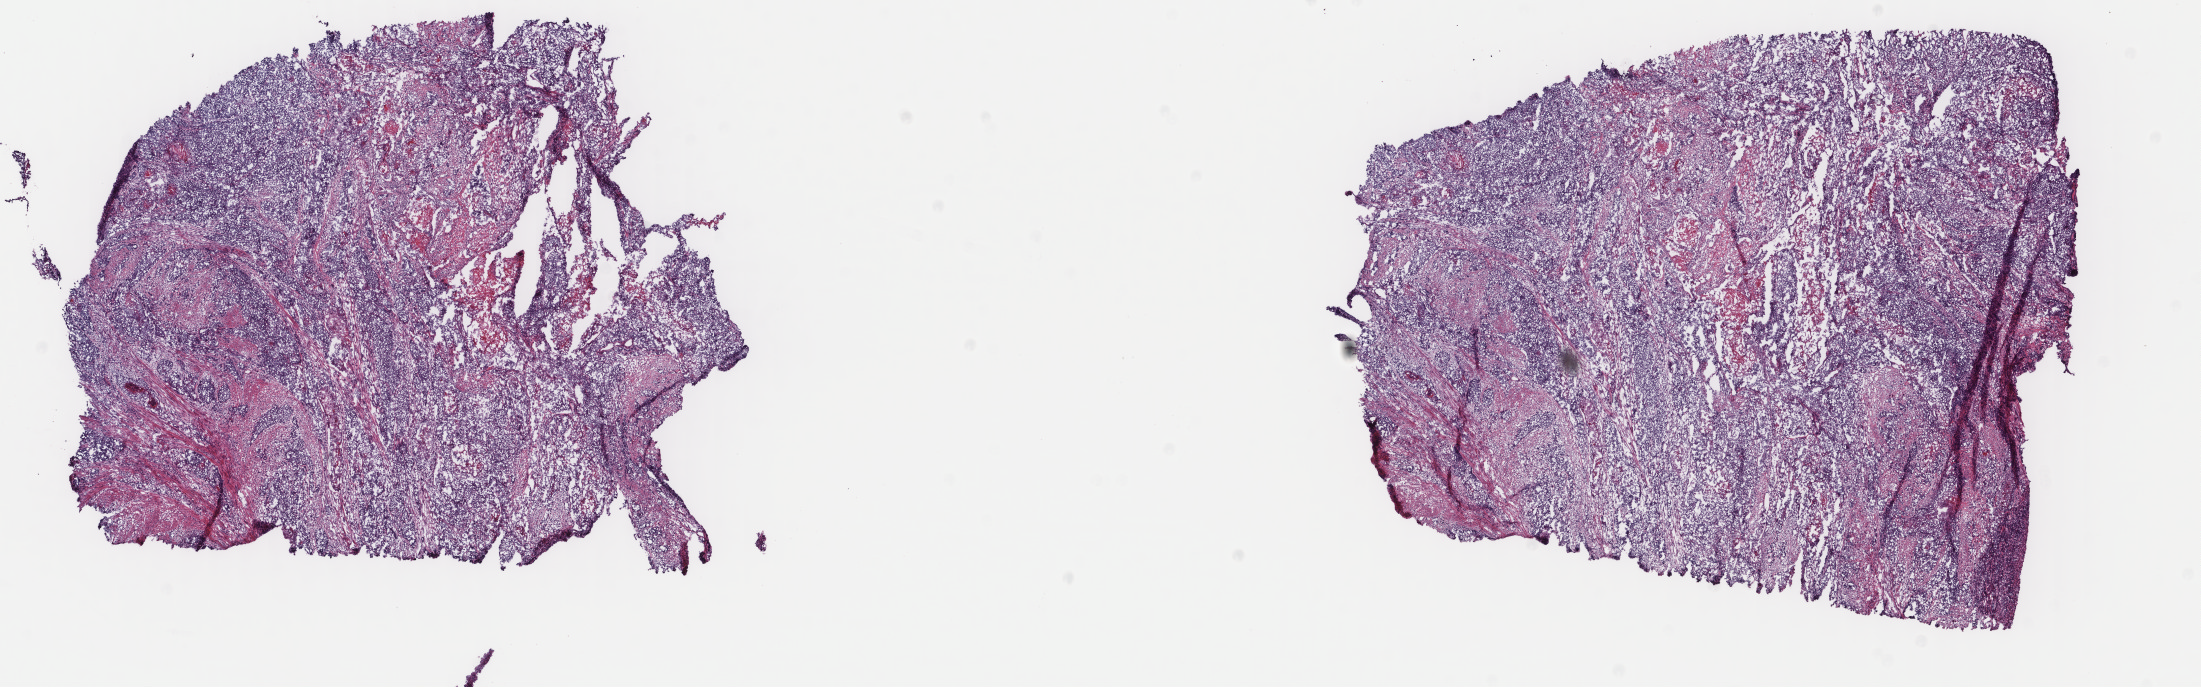
Hematoxylin and eosin (H&E) stained whole-slide image — whole scanned area (about 17.5 x 5.5 mm) shown as a low-resolution overview. Frozen section. Sample: primary tumour, uterus. Female, age 54 years at initial diagnosis. Histologic grade: G3 (poorly differentiated). Slide review estimates, as recorded: tumour cells 70%, tumour nuclei 70%, normal cells 0%, stromal cells 20%, necrosis 10%. Infiltration values recorded for this section: lymphocyte infiltration 40%, monocyte infiltration 20%, neutrophil infiltration 30%.
Histologic diagnosis: Endometrioid adenocarcinoma, NOS (endometrium). FIGO stage: IB. Lymph nodes positive (case pathology): 0 of 19 examined.